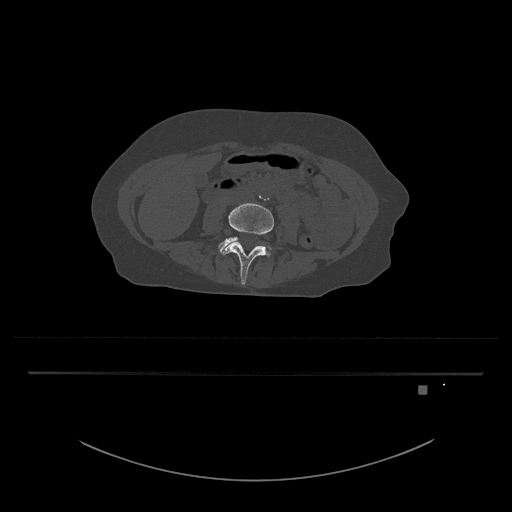
CT including the spine, one axial slice; position 352 of 797 along the scan axis; 120 kVp; bone window (W 1800 / L 400 HU); 0.5 mm slice thickness; 512 × 512 image matrix, field of view 500 × 500 mm. Female patient, age 57 years. From the clinical record (not read from this slice): primary cancer: cervical.
Annotated regions visible in this slice (semi-automatic segmentation, software-assisted and operator-edited):
- L4 vertebra: bounding box <221,203,274,285> (left, top, right, bottom; pixels)